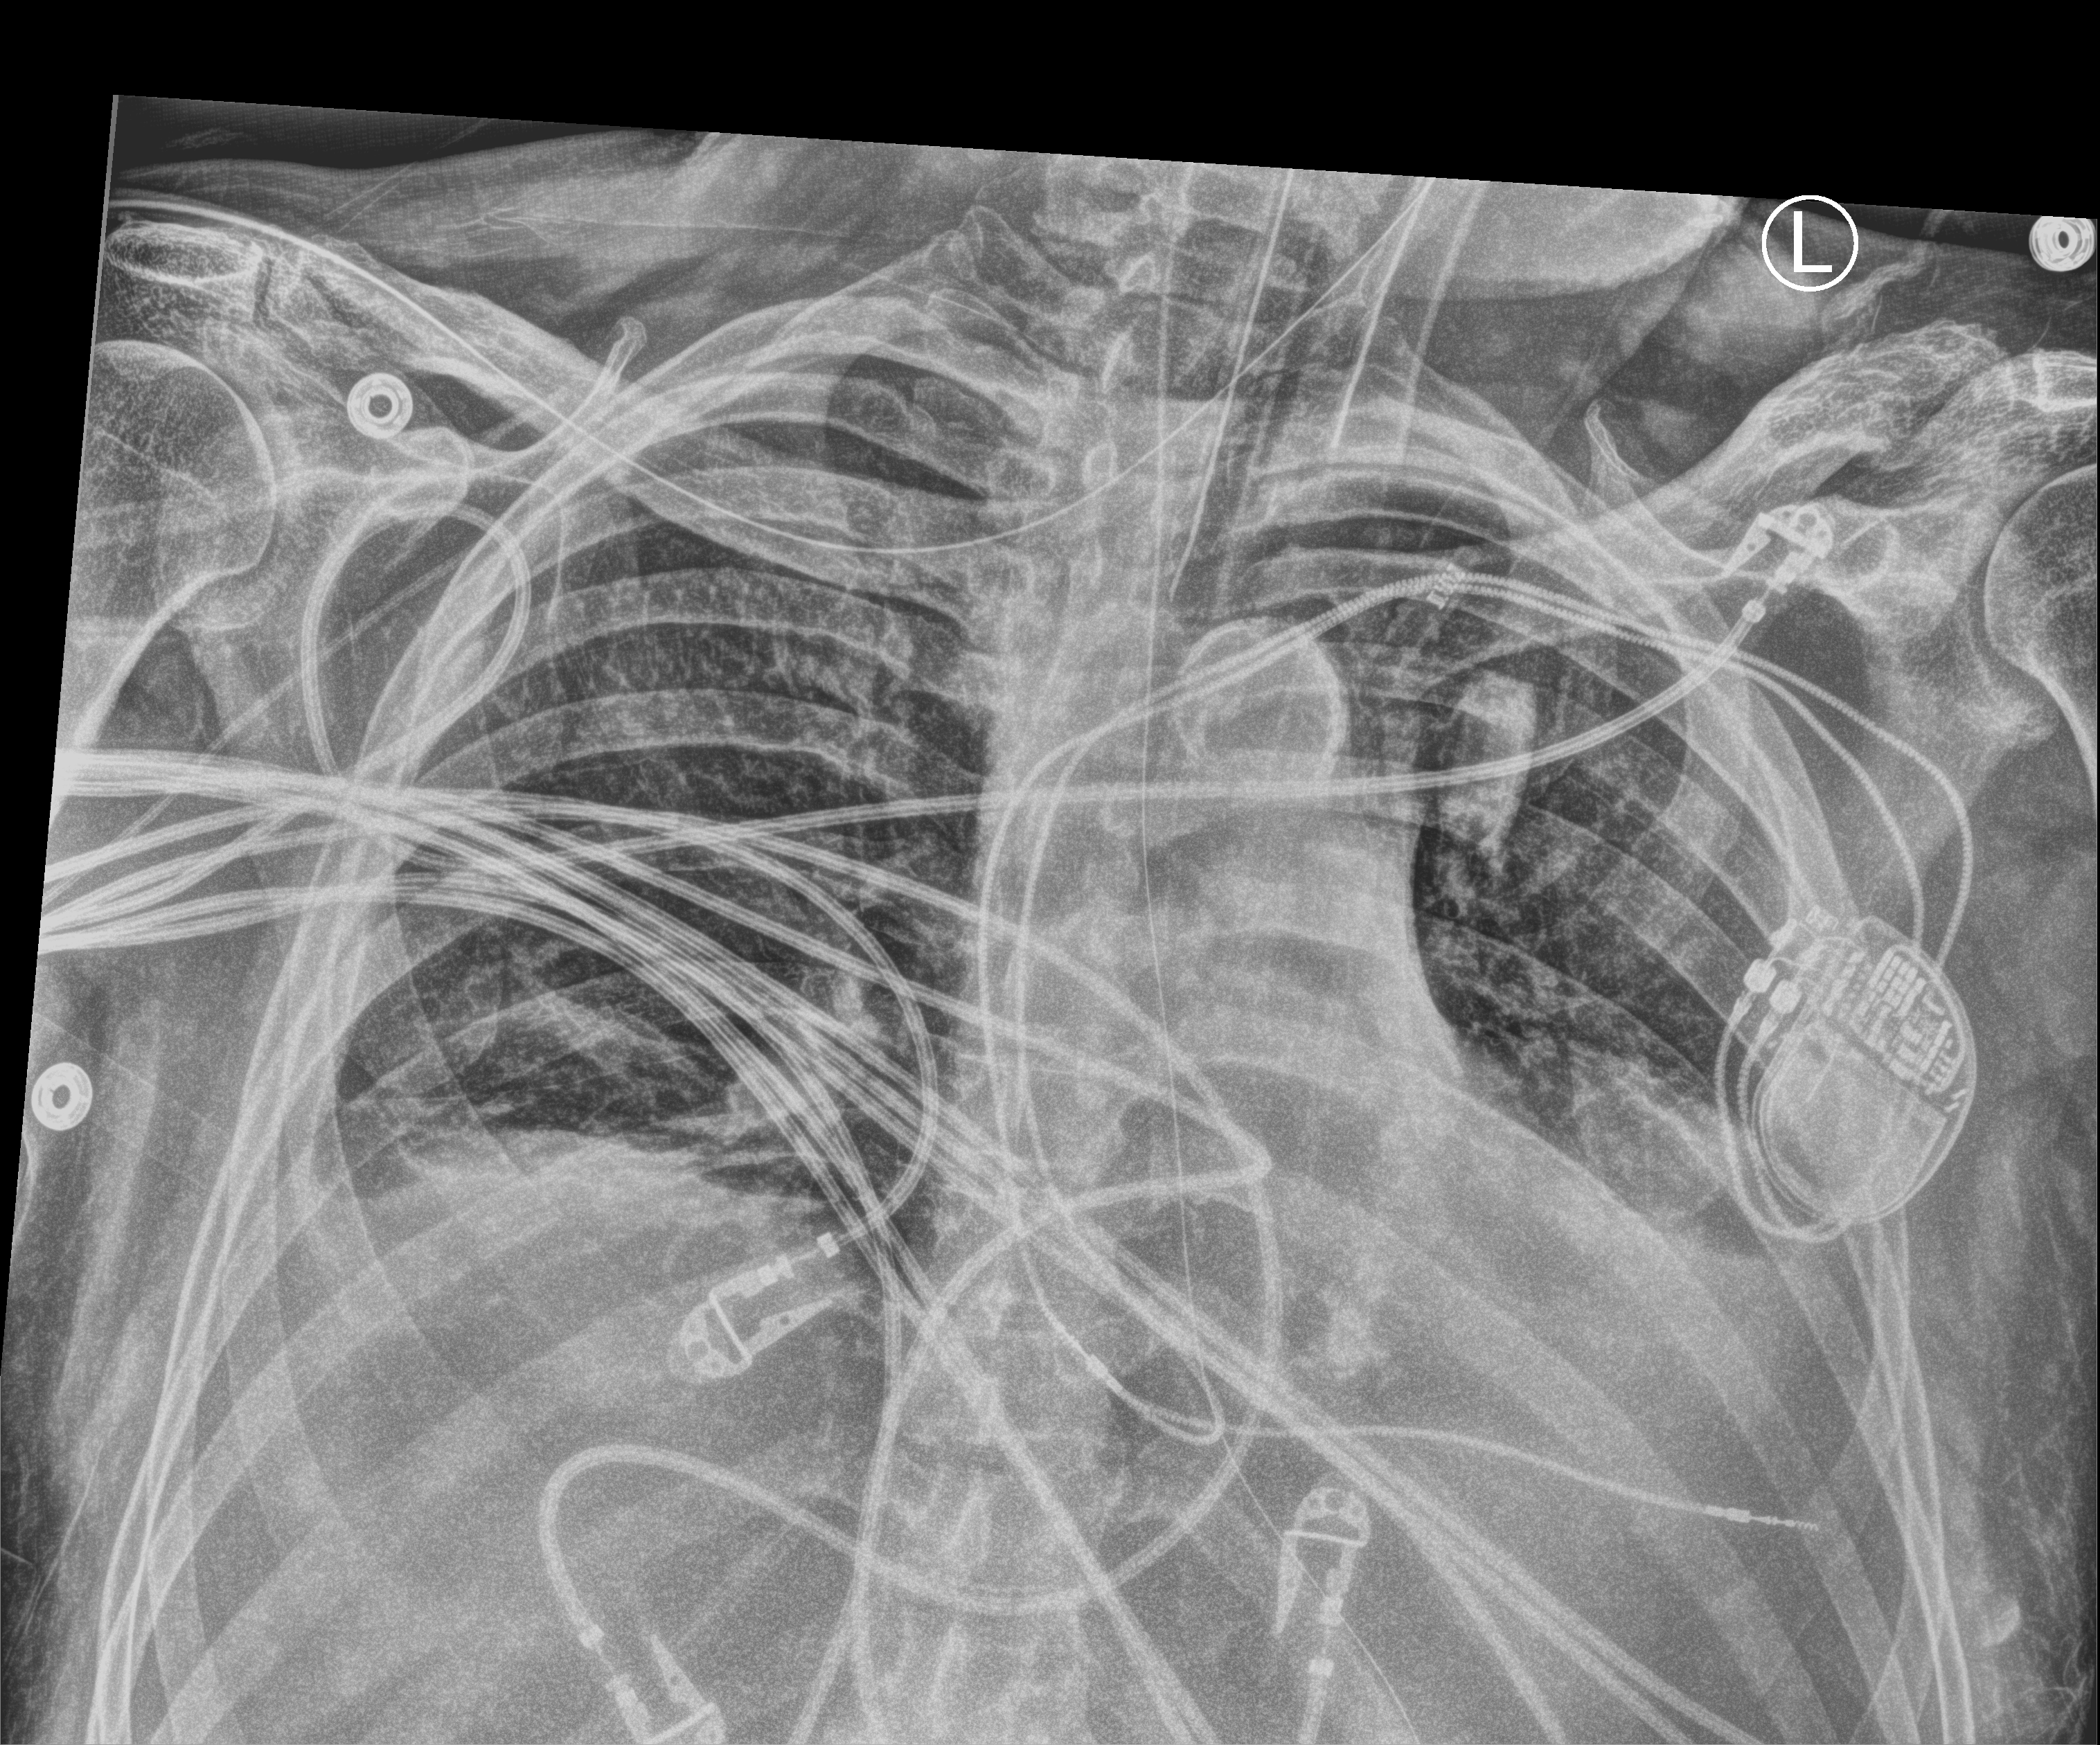
Bedside chest radiograph (computed radiography); anteroposterior (AP) projection. Patient hospitalised with COVID-19; male, aged 60–74 years.
Hospital-stay facts (about this admission, not read from this image; timing relative to this image not recorded): admitted to intensive care during this hospital stay: yes; mechanically ventilated during this hospital stay: yes; length of hospital stay: 41 days.